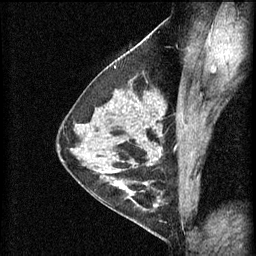
Breast MRI (dynamic contrast-enhanced), one sagittal slice; position 37 of 60 along the scan axis; 3 images stored at this slice position (order not interpretable as contrast timing); 1.5 T; TE 4.2 ms, TR 11 ms; 2 mm slice thickness; 256 × 256 image matrix. Female patient, age 29 years.
Annotated regions visible in this slice (semi-automatically segmented with operator editing):
- analysis volume of interest (the breast-tissue region the enhancement analysis was run in; not a lesion): box from (x=105, y=172) to (x=168, y=227) px
- tumour enhancement mask (voxels above the 70 % enhancement threshold inside the analysis volume of interest): (x=111, y=172)–(x=162, y=211)